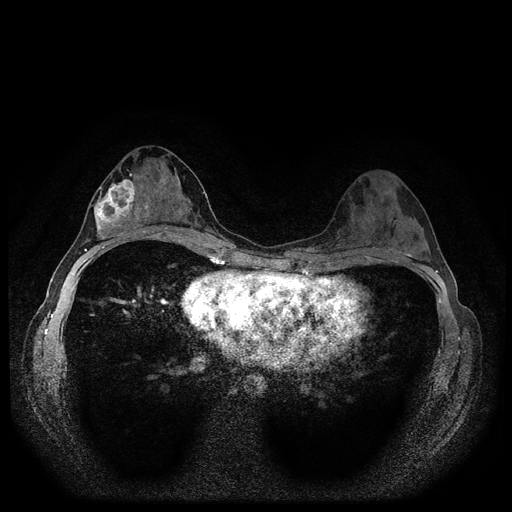
Breast MRI (dynamic contrast-enhanced, multi-phase), one axial slice. Slice 56 of 116 in the series (ordered by position). Dynamic contrast-enhanced series, time point 2 of 5 at this slice position (early post-contrast). 1.5 T. TE 2.7 ms, TR 5.4 ms. 512 × 512 image matrix, field of view 320 × 320 mm. Female patient, age 29 years.
Outlined on this slice (semi-automatically segmented with operator editing):
- breast lesion (labelled 'tumour' in the annotation; benign lesions carry a separate 'benign' label): bounding box (x1, y1, x2, y2) in pixels: (91, 174, 141, 239)